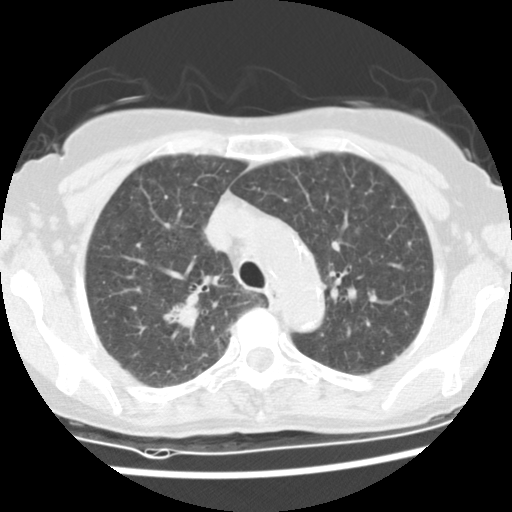
Axial slice from a low-dose chest CT screening exam; first (baseline) screen; lung window (W 1500 / L -600 HU); 2.5 mm slice thickness; standard (soft-tissue) reconstruction kernel (STANDARD); slice 32 of 134 in the series; 512 × 512 image matrix. Female participant, aged 66 years at enrolment.
- Expert-annotated lung lesion, box from (x=150, y=291) to (x=201, y=335) px.
- Reader record for this screening exam (exam-level; its link to the box is not recorded): non-calcified nodule or mass ≥4 mm, right upper lobe, 13 × 11 mm, soft tissue attenuation.
- Official screen result: positive, change unspecified: nodule(s) >= 4 mm or enlarging nodule(s), mass(es), or other non-specific abnormalities suspicious for lung cancer.
- Participant outcome: lung cancer diagnosed 64 days after this screen — adenocarcinoma, NOS, right upper lobe, poorly differentiated (G3), stage IA (AJCC 6th edition), 18 mm at pathology.